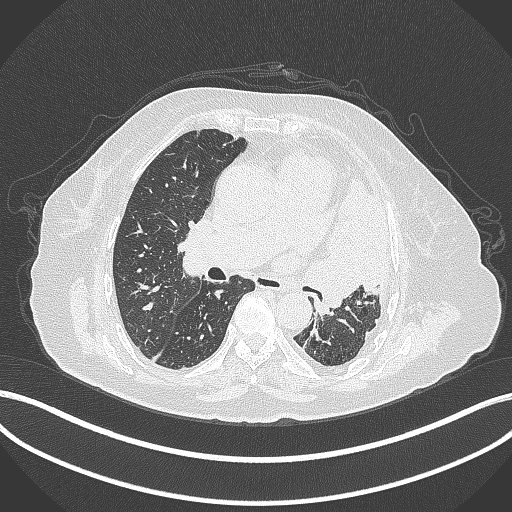
Chest CT, one axial slice; position 208 of 399 along the scan axis; reconstruction kernel B70f; lung window (W 1500 / L -600 HU); 1 mm slice thickness; 512 × 512 image matrix, field of view 400 × 400 mm. Patient: female, 75 years. Case-level facts recorded for this patient, not image findings: clinical TNM (as recorded): T3 N3 M1.
Structures marked on this image (bounding box drawn by a radiologist):
- lung tumour (recorded histology: adenocarcinoma): box from (x=298, y=166) to (x=395, y=311) px